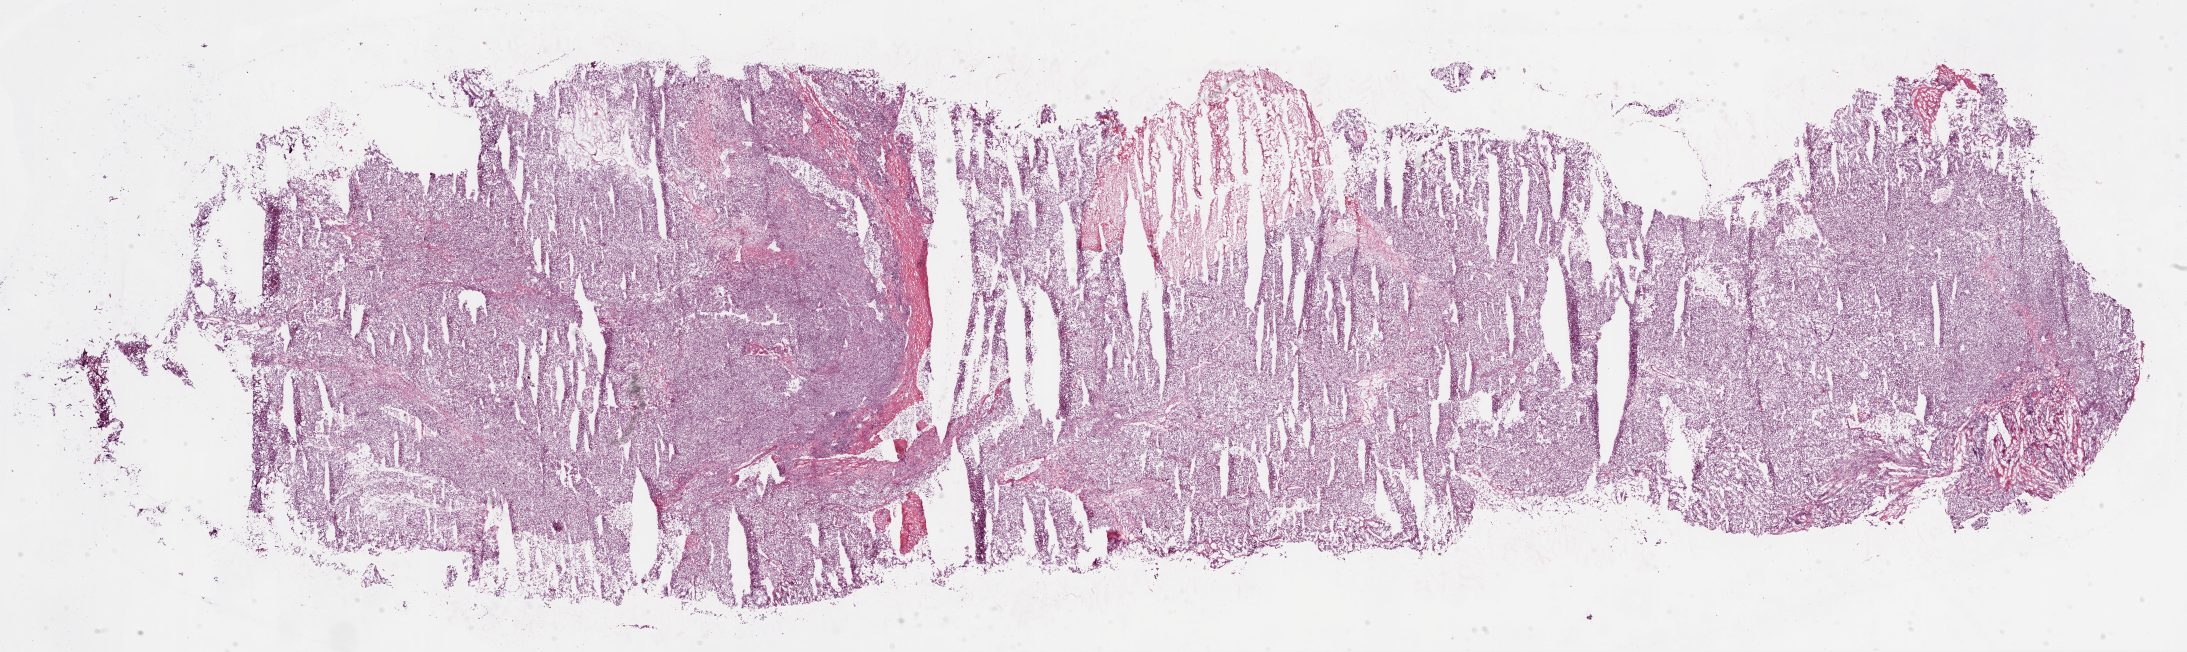
Digitized Hematoxylin and eosin (H&E) stained tissue section (whole slide), low-resolution overview of the scanned area, about 35.1 x 10.5 mm (slide scanned at 20x); frozen section from the bottom of the tissue portion; primary tumour sample from the kidney. Female patient. Histologic grade: G3 (poorly differentiated). Composition of this section per pathologist review: tumour cells 90%, tumour nuclei 90%, normal cells 0%, stromal cells 10%, necrosis 0%.
• diagnosis: Clear cell adenocarcinoma, NOS
• lymph nodes positive (case pathology): 0 of 3 examined
• AJCC pathologic stage: III
• TNM: T3a N0 M0
• laterality: right